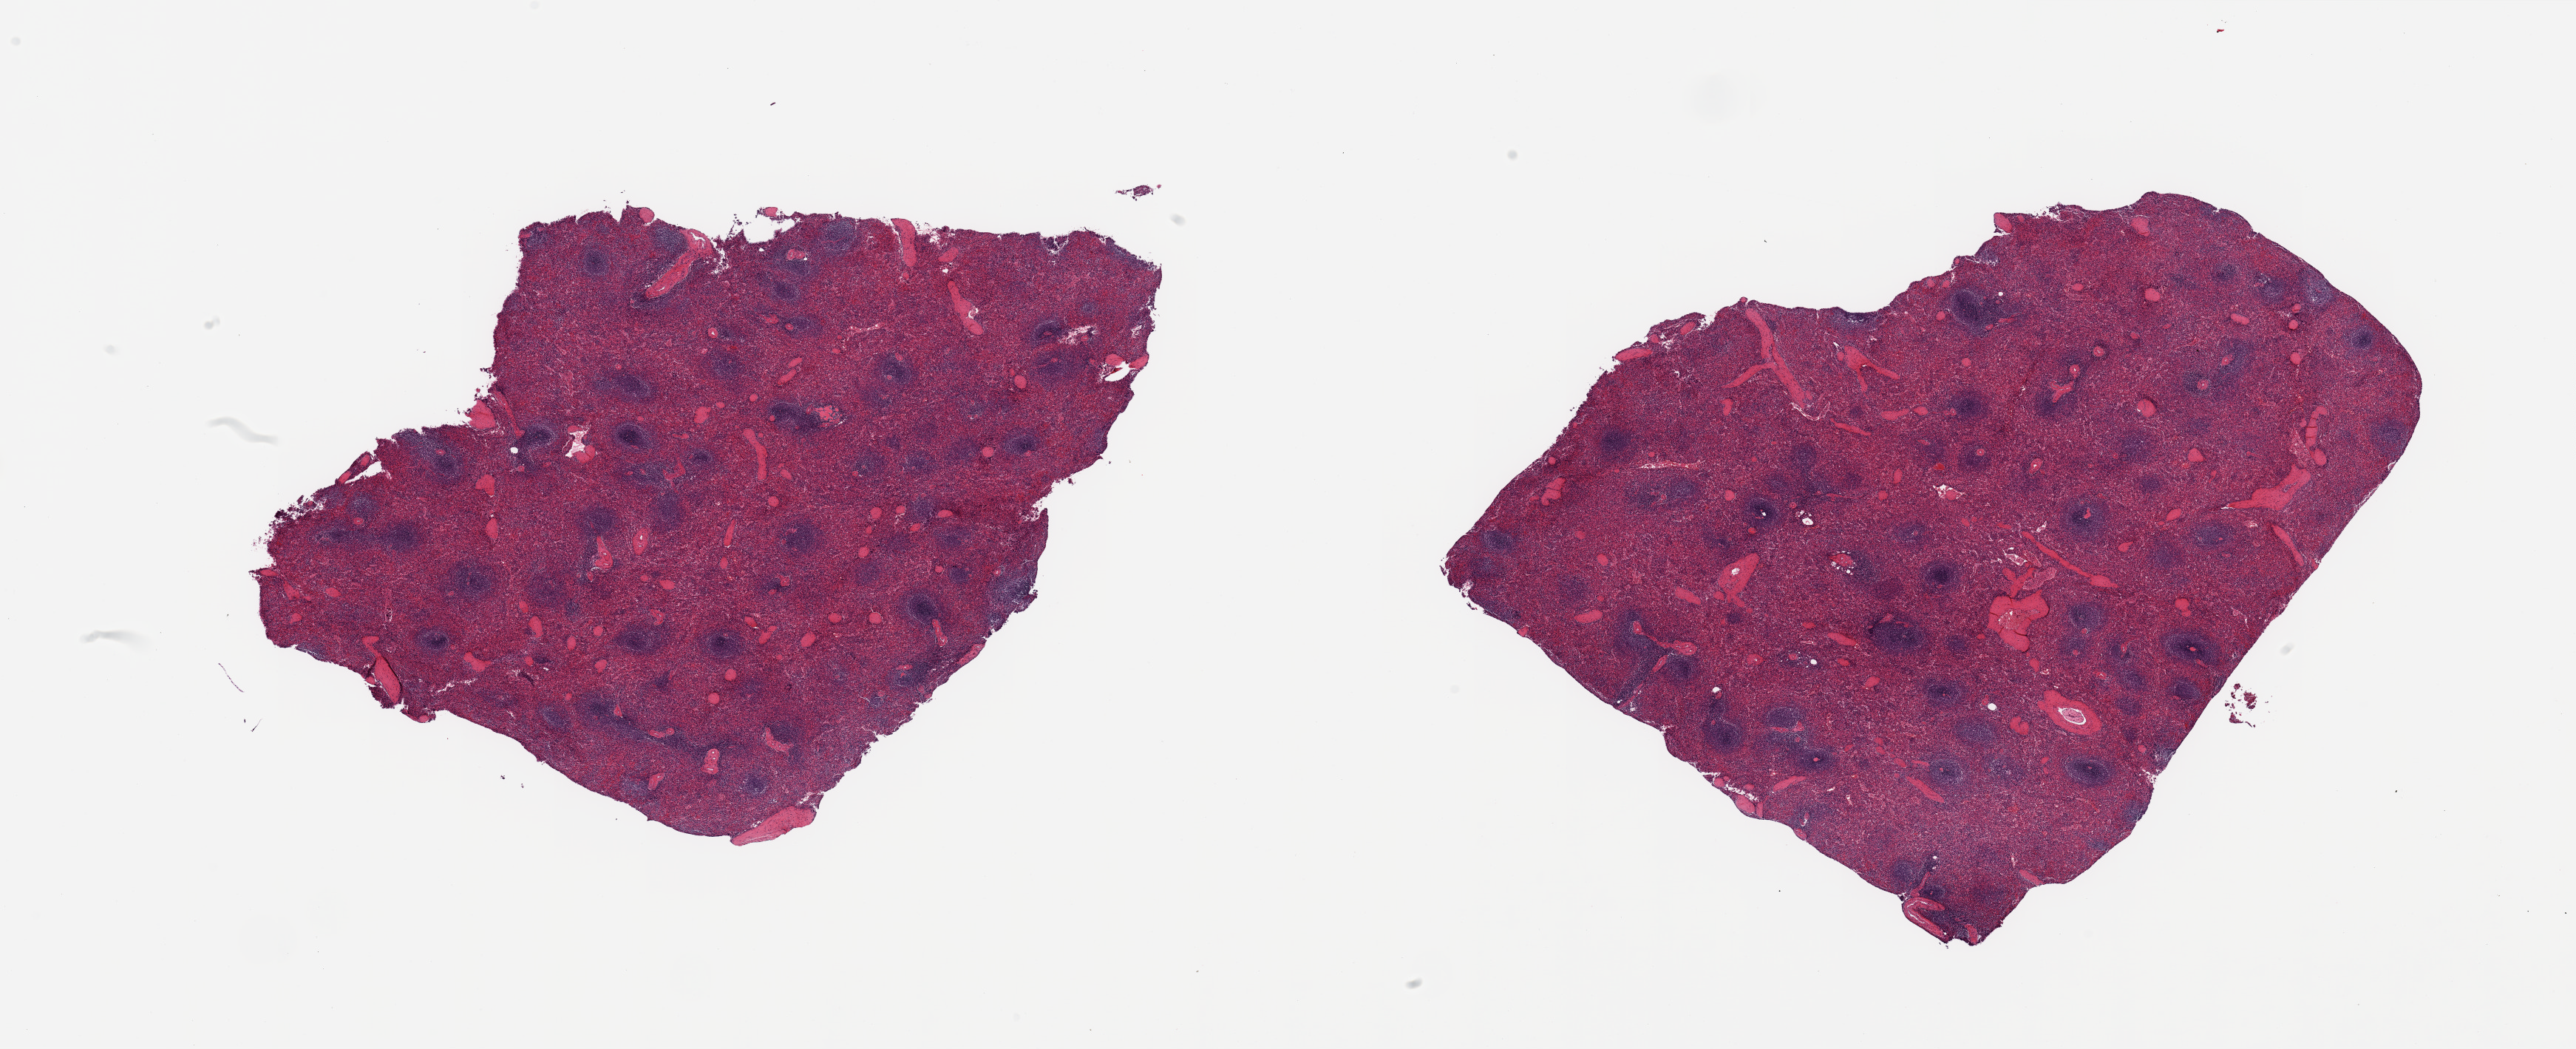
H&E whole-slide image, brightfield — shown as a low-resolution overview of the whole scanned area (about 27.6 x 11.2 mm, acquisition: 20x scan); PAXgene-fixed, paraffin-embedded tissue; section of spleen (target tissue); donor tissue sample. Male donor.
Reviewer comment on this tissue sample: 2 pieces, no abnormalities.